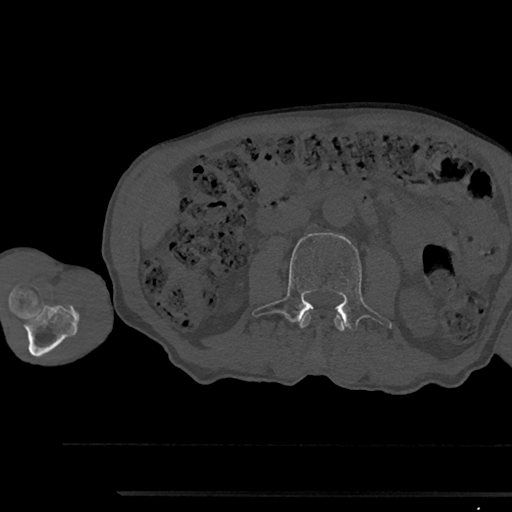
CT including the spine, one axial slice; slice 505 of 797 in the series (ordered by position); reconstruction kernel Br40s/3; 120 kVp; bone window (W 1800 / L 400 HU); 0.5 mm slice thickness; 512 × 512 image matrix, field of view 367 × 367 mm. Male patient, age 79 years. Case-level facts recorded for this patient, not image findings: primary cancer: prostate.
Annotated regions visible in this slice (semi-automatically segmented with operator editing):
- L2 vertebra: bounding box (x1, y1, x2, y2) in pixels: (299, 315, 345, 331)
- L3 vertebra: (252, 233, 393, 328)